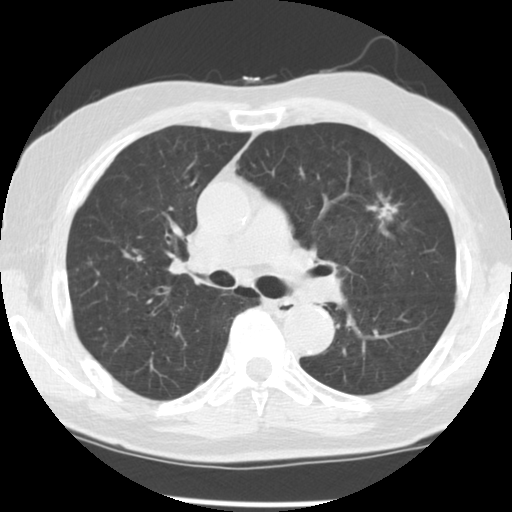
Low-dose screening chest CT, axial slice. Third annual screen. Lung window (W 1500 / L -600 HU). 2.5 mm slice thickness. Slice 79 of 131 in the series. 512 × 512 image matrix. Male participant, aged 70 years at enrolment. Current smoker at enrolment.
Expert reader's lesion annotation, bounding box <356,185,413,243> (left, top, right, bottom; pixels). The screening reader recorded 3 non-calcified nodules or masses ≥4 mm on this exam; which of them this box marks is not recorded. Participant outcome: lung cancer diagnosed 74 days after this screen — adenocarcinoma, NOS, left upper lobe, moderately differentiated (G2), stage IIIA (AJCC 6th edition), 17 mm at pathology.